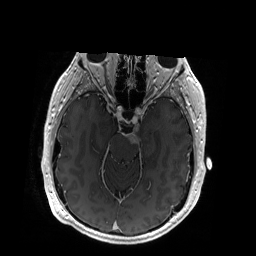
Brain MRI from a brain-tumour surgery series, one axial slice; slice 120 of 192 in the series (ordered by position); T1-weighted post-contrast; 1 mm slice thickness; 256 × 256 image matrix, field of view 256 × 256 mm. From the clinical record (not read from this slice): histopathology: Glioblastoma; WHO grade: 4; IDH mutation: no.
Structures marked on this image (outlined manually by an expert reader):
- tumour: box from (x=126, y=125) to (x=142, y=144) px